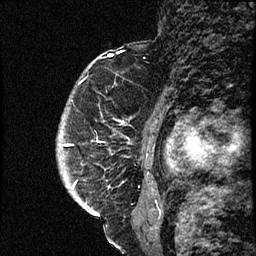
Breast MRI (dynamic contrast-enhanced), one sagittal slice. Position 54 of 66 along the scan axis. Dynamic contrast-enhanced study with each time point stored as its own series, time point 2 of 3 at this slice position (early post-contrast, ordered by acquisition time). 1.5 T. TE 4.2 ms, TR 17.6 ms. 256 × 256 image matrix. Female patient. Case-level facts recorded for this patient, not image findings: setting: breast cancer imaged before/during neoadjuvant chemotherapy; receptor status: HER2-positive.
Annotated regions visible in this slice (semi-automatically segmented with operator editing):
- analysis volume of interest (the breast-tissue region the enhancement analysis was run in; not a lesion): bounding box [x1, y1, x2, y2] px = [58, 69, 177, 209]
- tumour enhancement mask (voxels above the 100 % enhancement threshold inside the analysis volume of interest): [59, 121, 177, 209]